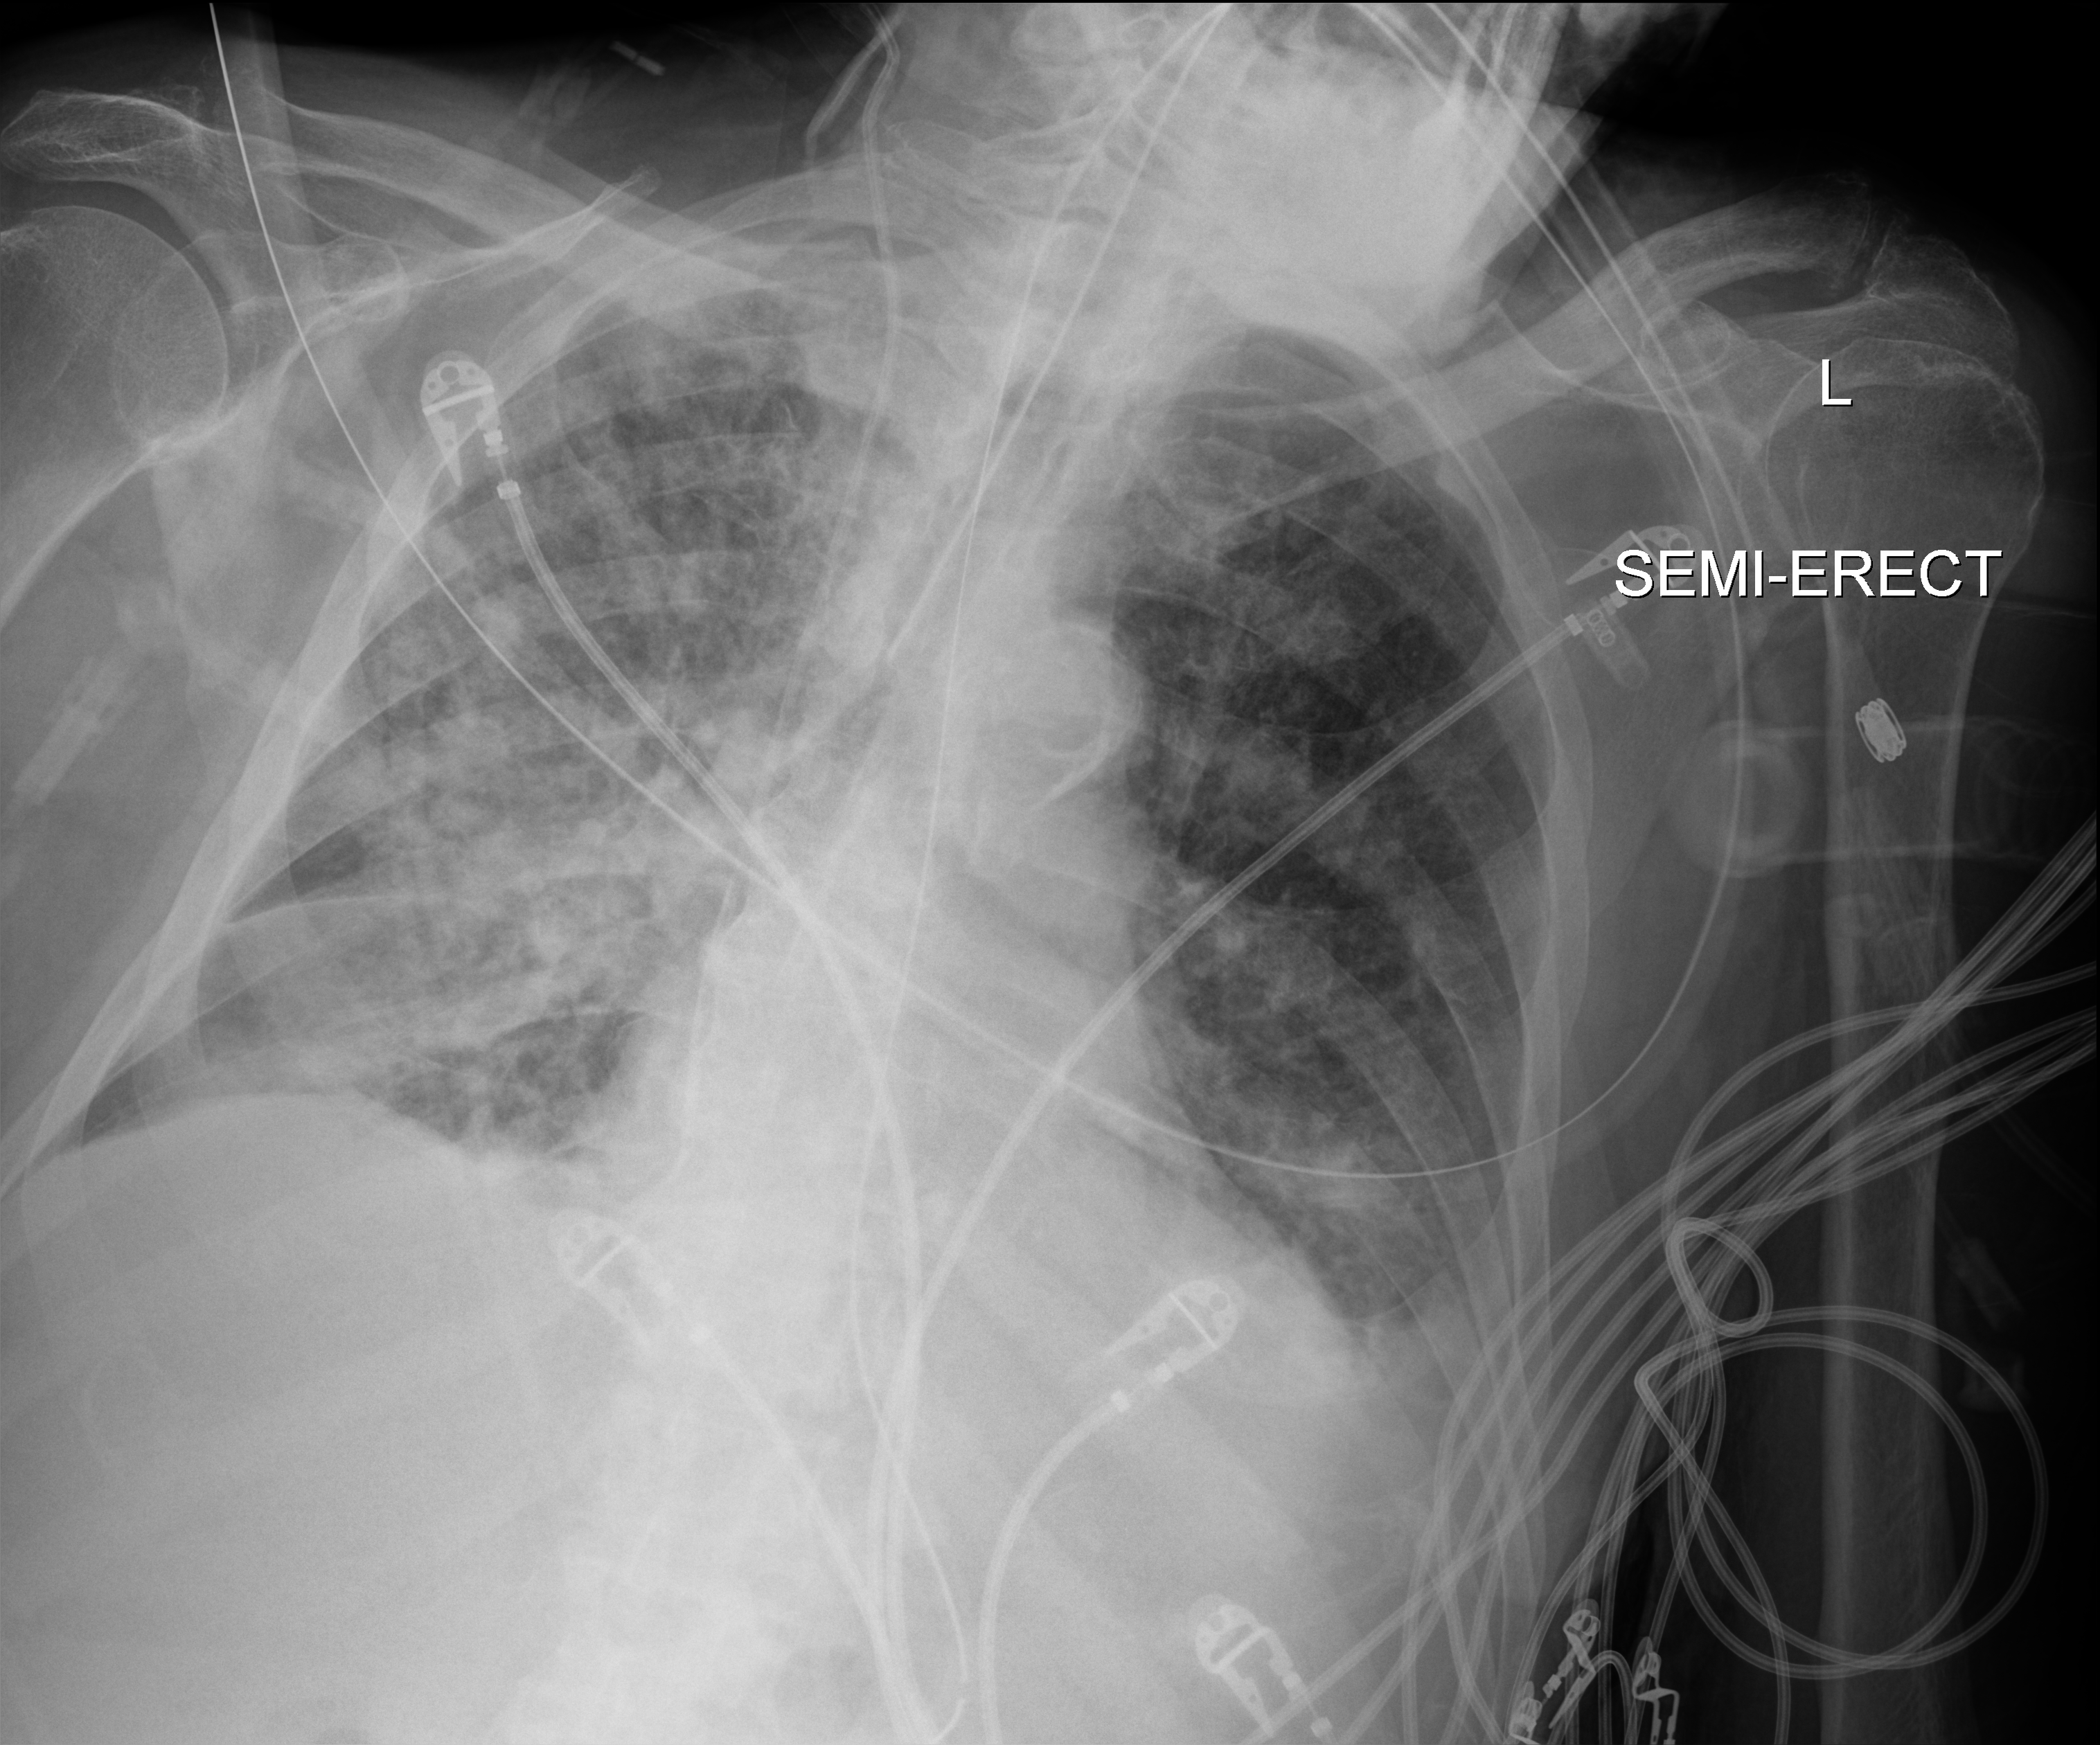
Portable chest radiograph; anteroposterior (AP) projection. Patient hospitalised with COVID-19; male, aged 75–90 years.
From the hospital-stay record, not from the radiograph (when in the stay this image was taken is not recorded):
- mechanically ventilated during this hospital stay: yes
- admitted to intensive care during this hospital stay: yes
- length of hospital stay: 28 days